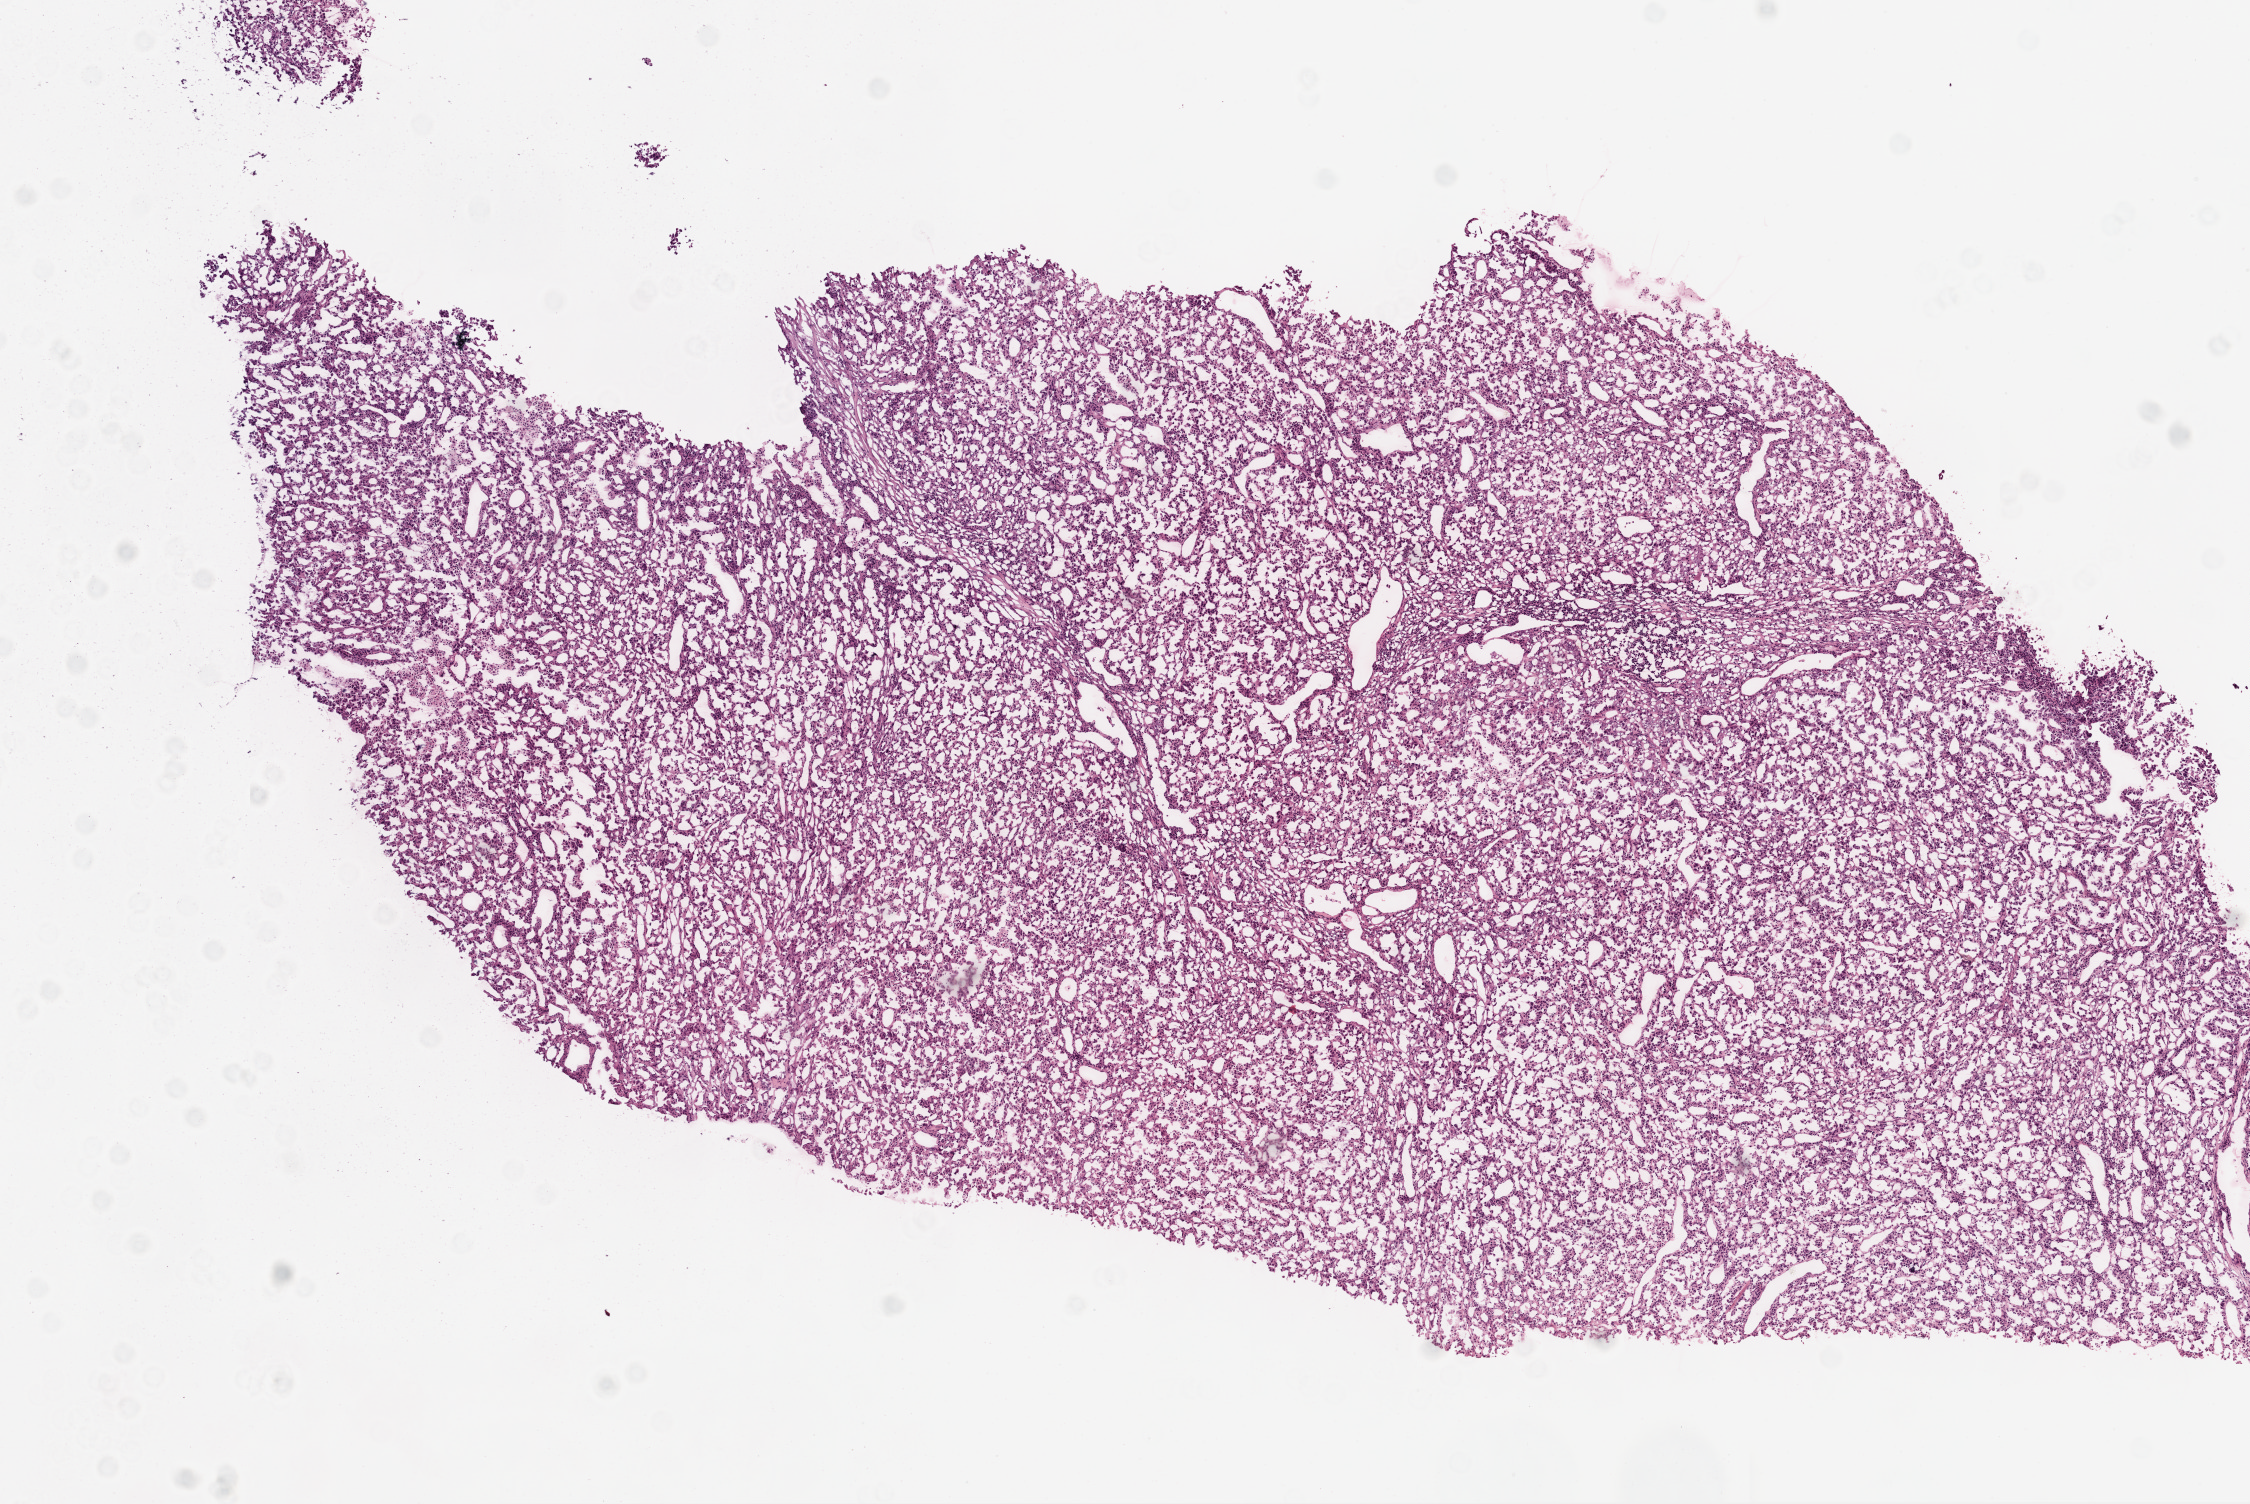
H&E whole-slide image — shown as a low-resolution overview of the whole scanned area (about 9.0 x 6.0 mm). Frozen section from the top of the tissue portion. Sample: primary tumour, lung. Female patient; age at initial diagnosis 73 years. Composition of this section per pathologist review: tumour cells 95%, tumour nuclei 70%, normal cells 0%, stromal cells 5%, necrosis 0%.
- AJCC pathologic stage: IIIA
- histologic diagnosis: Adenocarcinoma, NOS (main bronchus)